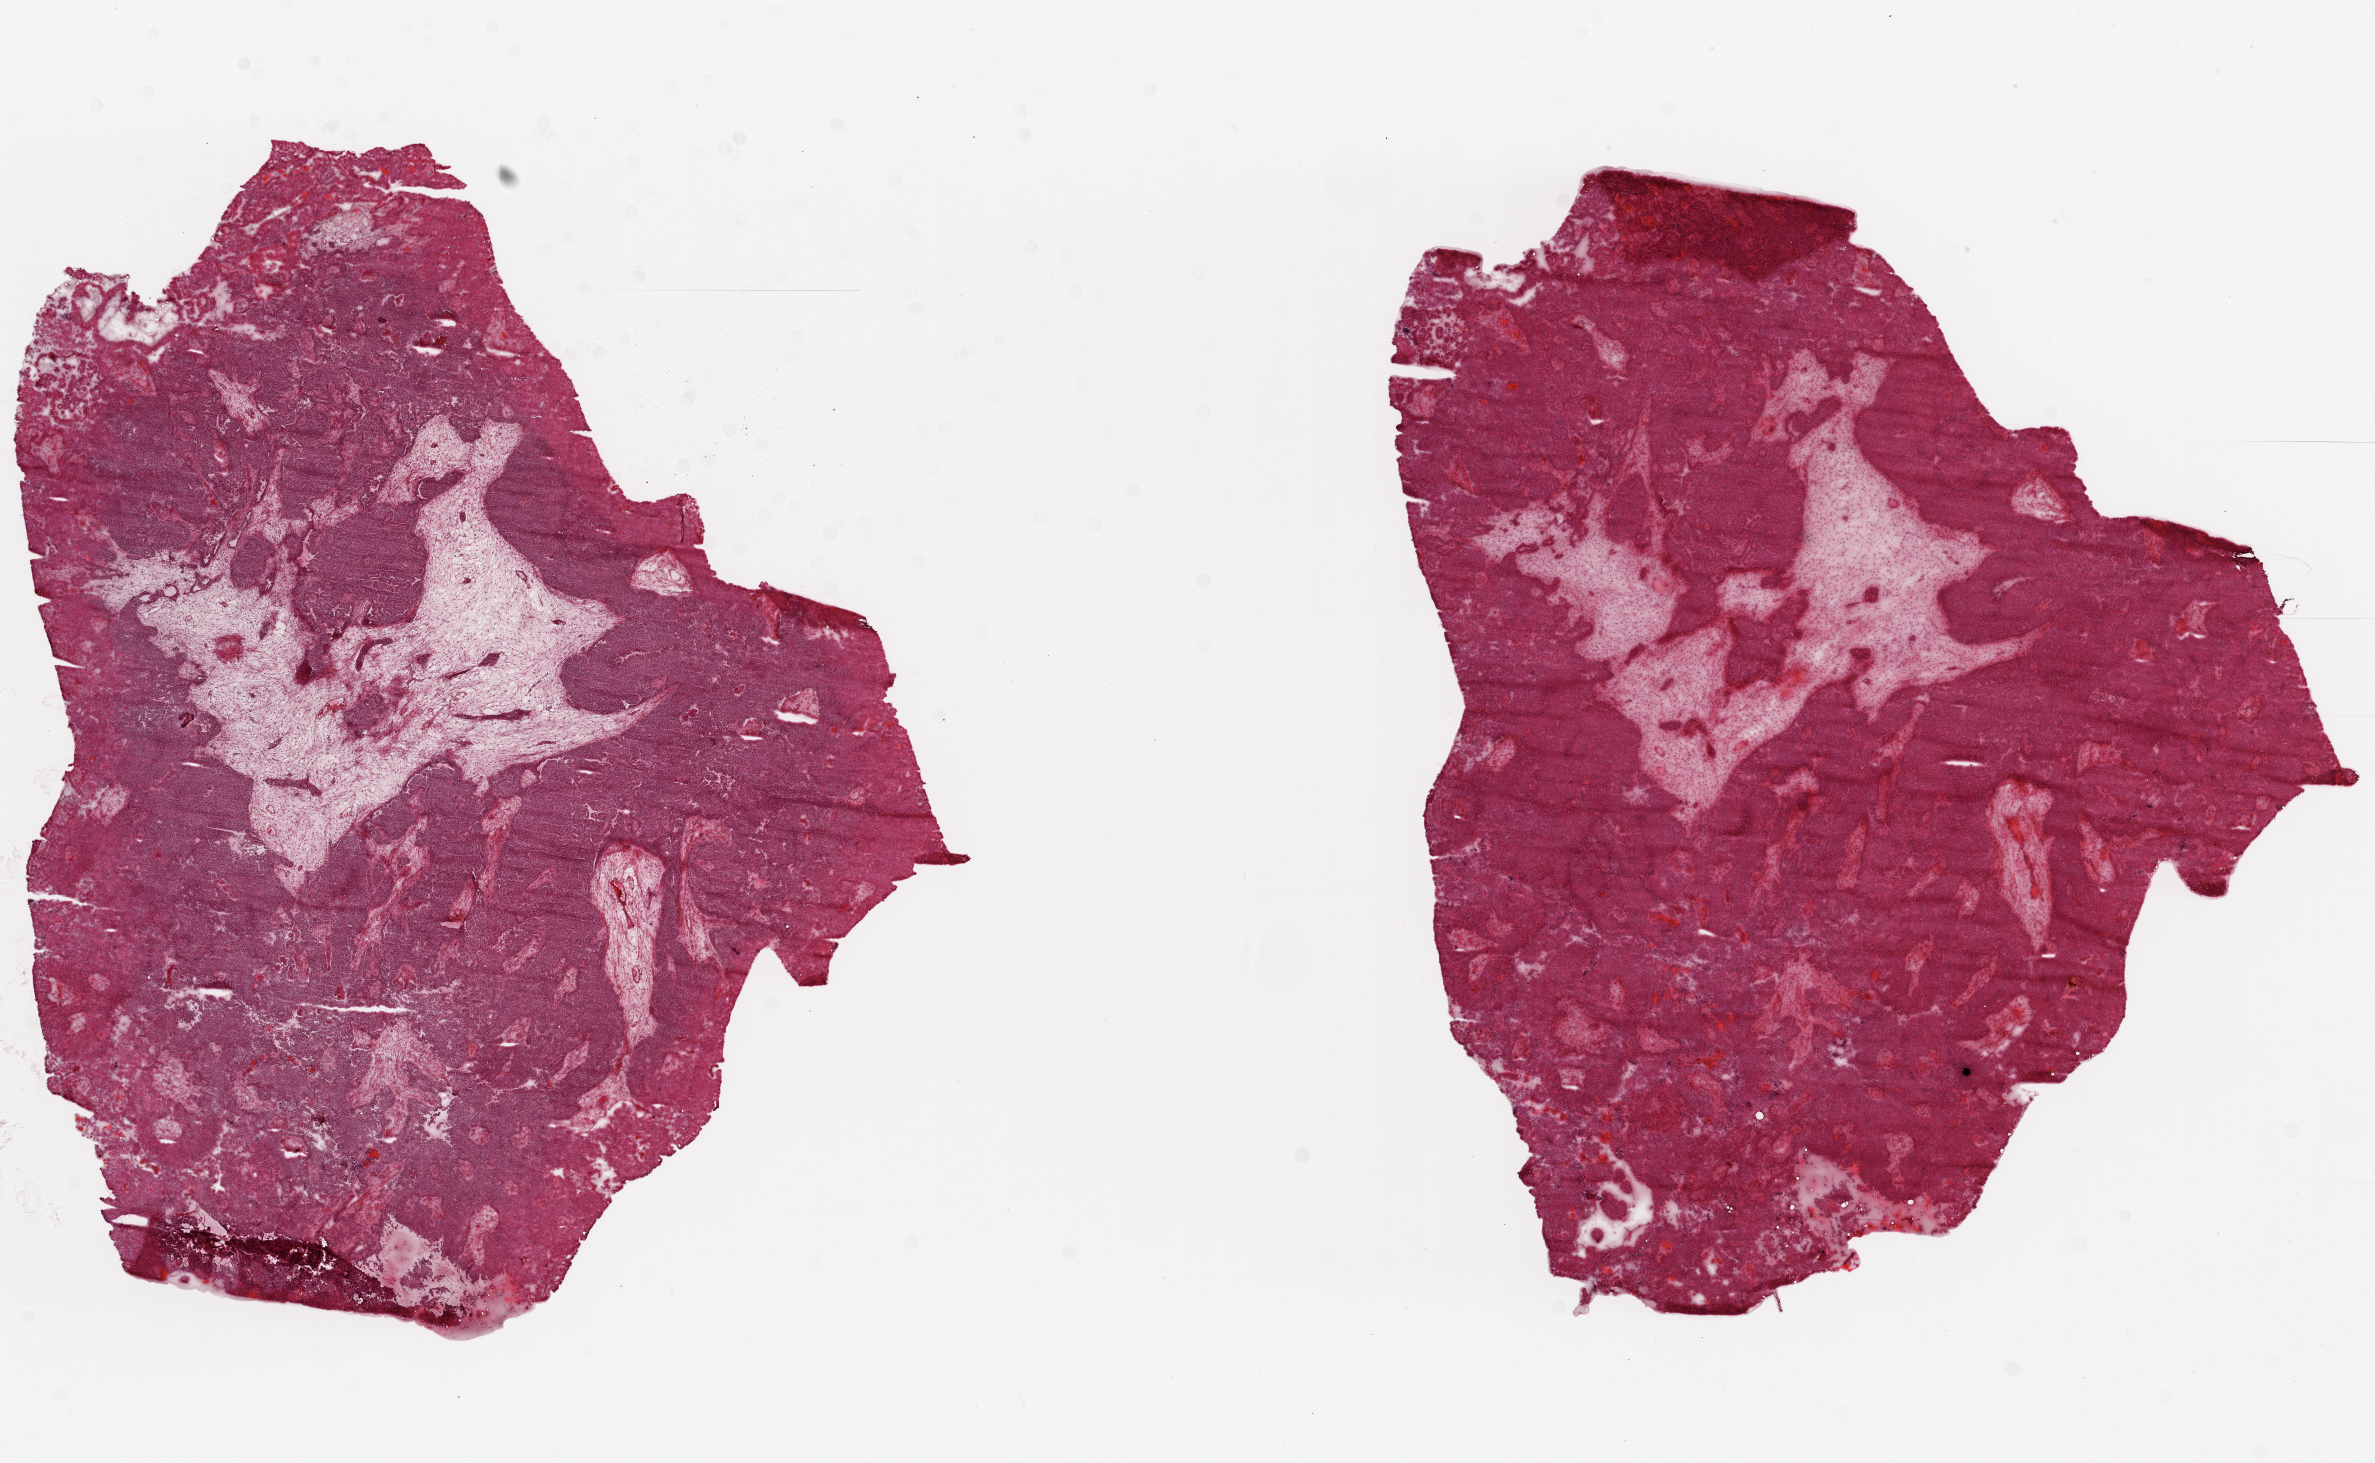
Whole-slide histology image, H&E-stained — whole scanned area (about 19.1 x 11.7 mm, acquisition: 20x scan) shown as a low-resolution overview, frozen section from the top of the tissue portion, sample: primary tumour, ovary. Female, age 62 years at initial diagnosis. Histologic grade: G3 (poorly differentiated). Pathologist review of this section (percent, as recorded): tumour cells 75%, tumour nuclei 95%, normal cells 25%, stromal cells 0%, necrosis 0%.
Diagnosis: Serous cystadenocarcinoma, NOS. FIGO stage: IIIC.